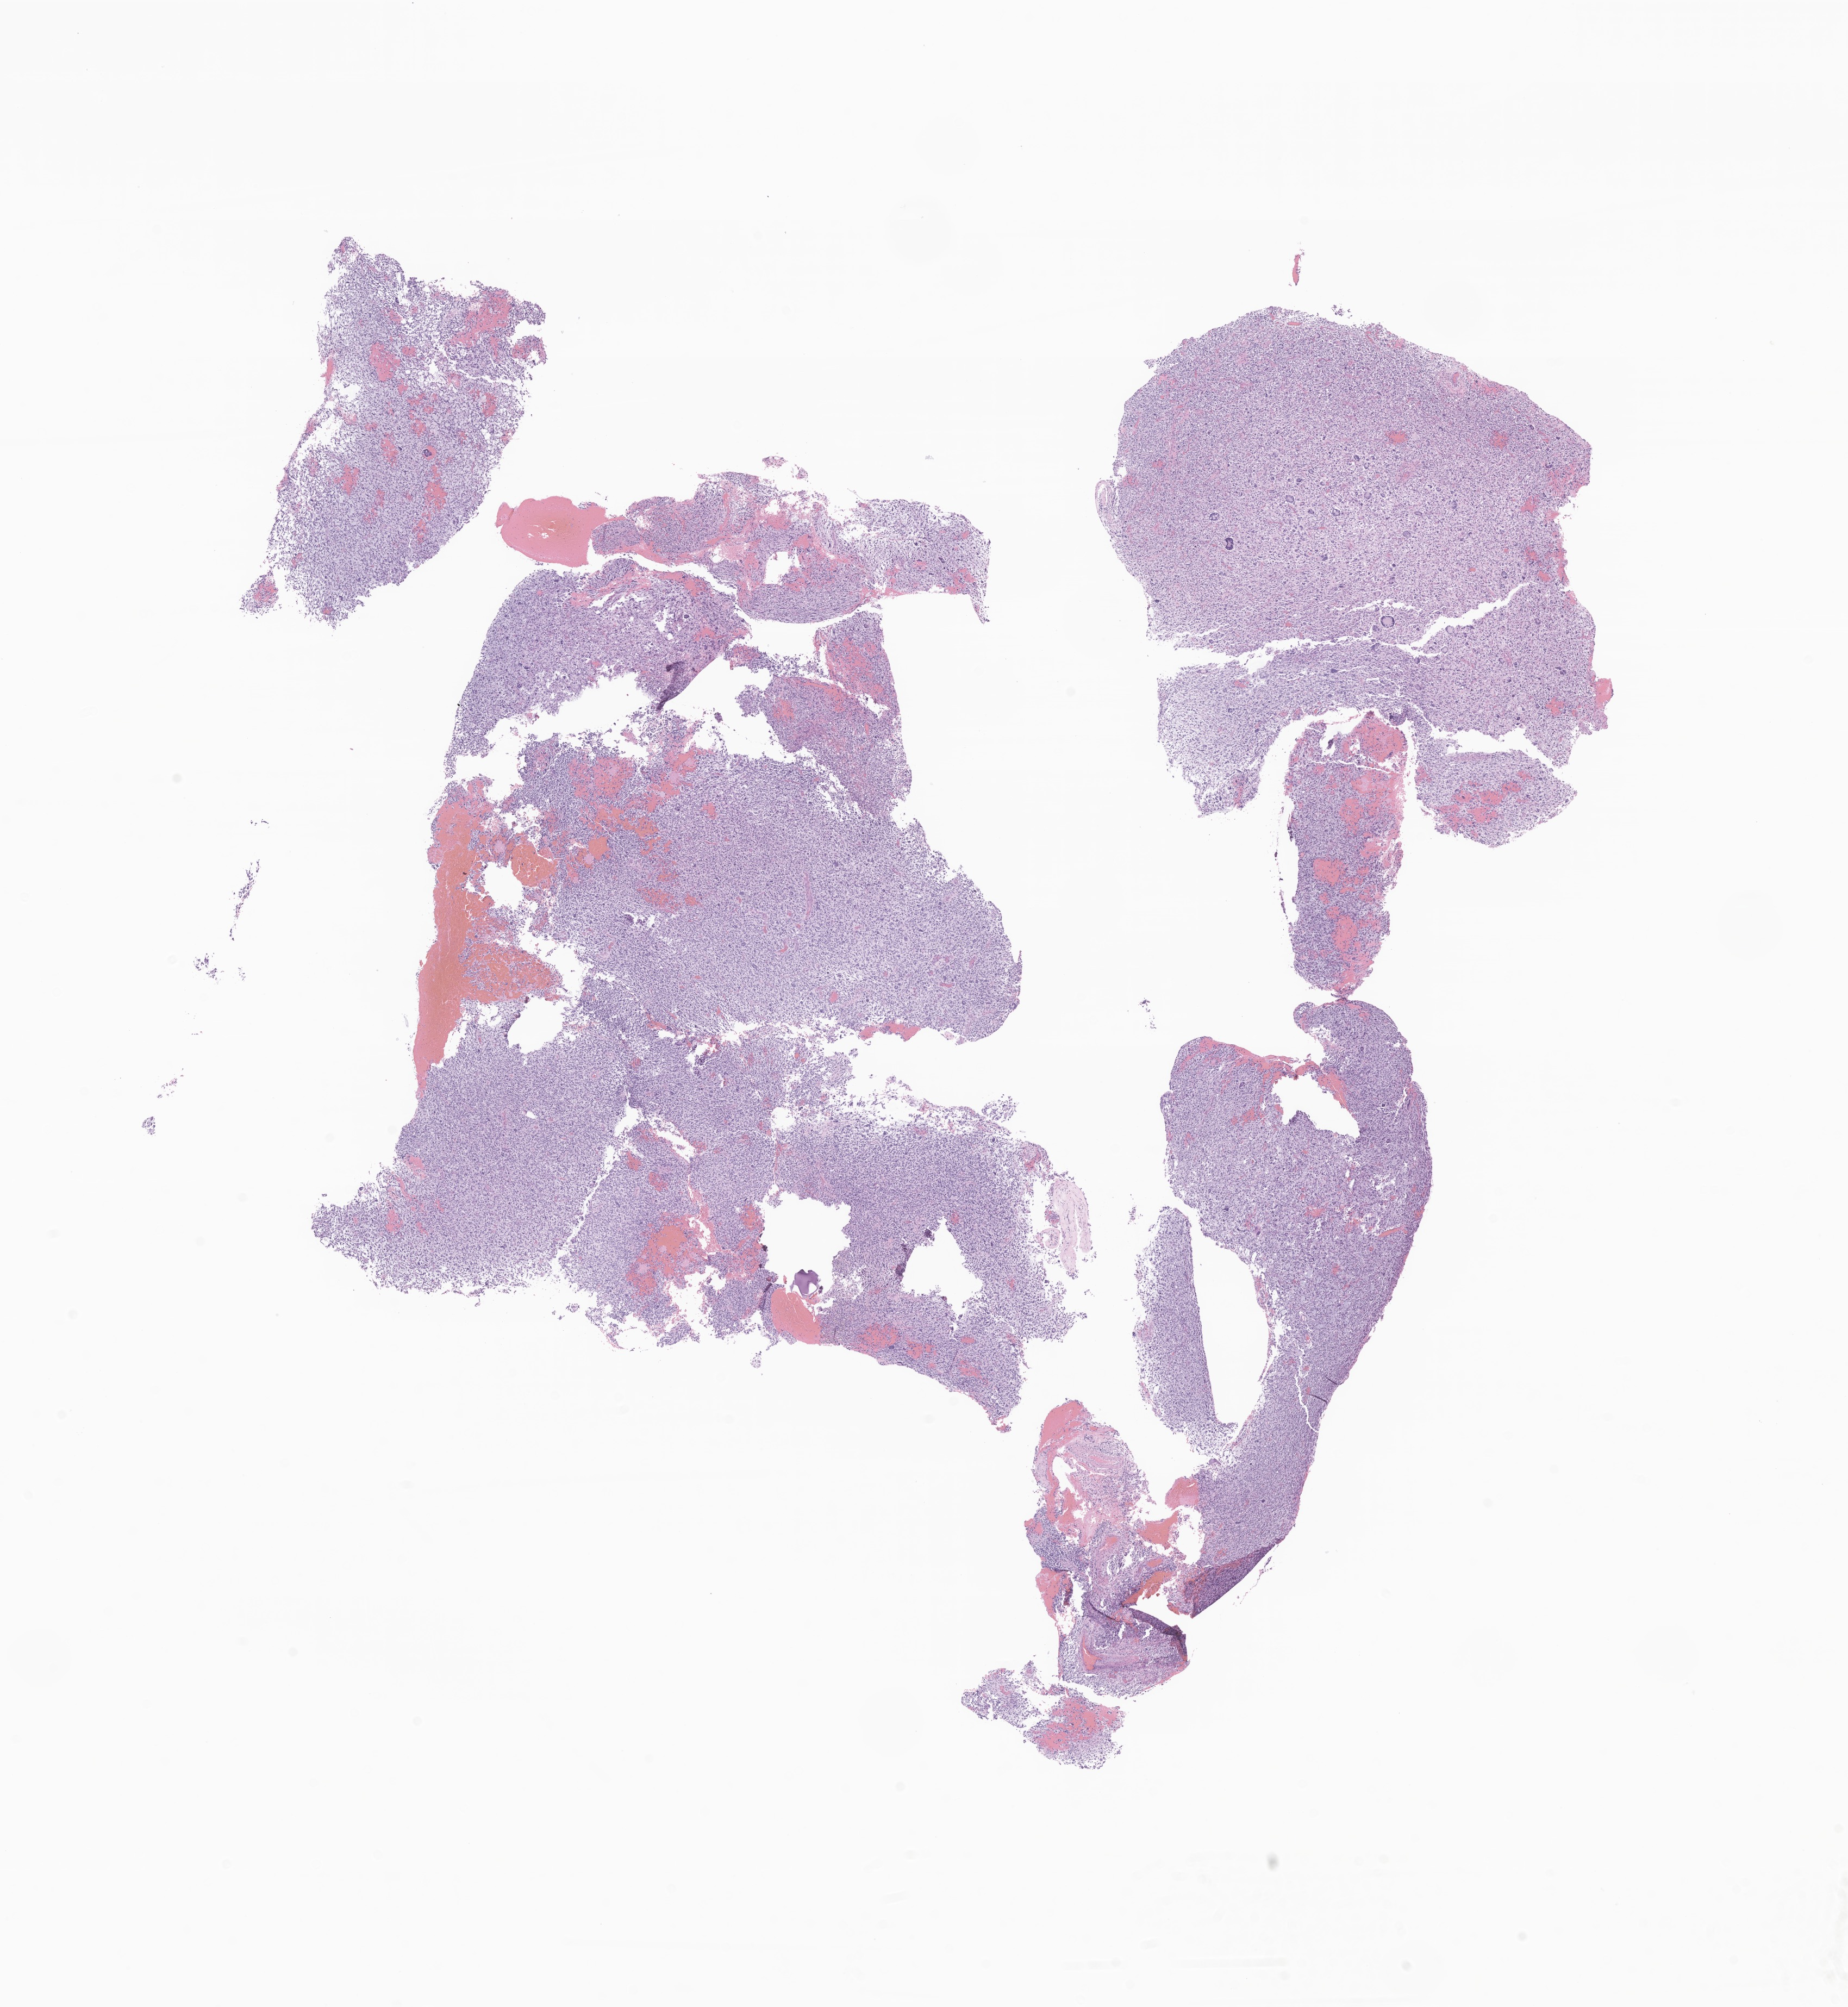
Whole-slide image, haematoxylin and eosin stain of tumor tissue from the brain, low-resolution overview of the scanned area, about 14.3 x 15.6 mm. FFPE section. Male patient, age 254 months (21 years 2 months).
Diagnosis (ICD-O-3 morphology term): Glioma, malignant.